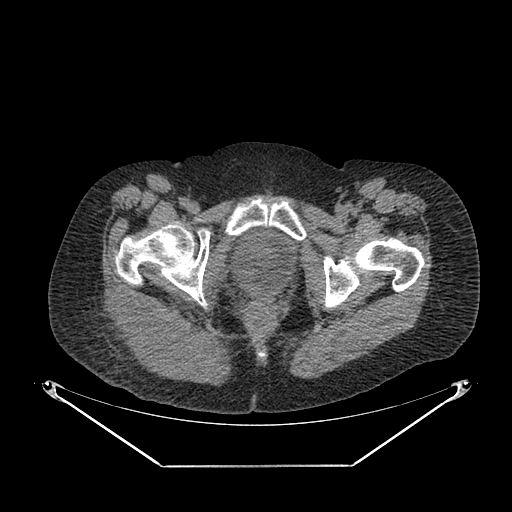
CT of an extremity soft-tissue mass (from a PET/CT study), one axial slice; position 49 of 267 along the scan axis; 140 kVp; soft-tissue window (W 400 / L 40 HU); 512 × 512 image matrix, field of view 500 × 500 mm. Female patient. From the clinical record (not read from this slice): histological type: spindle cell suggestive of myxofibrosarcoma; grade: intermediate; site of the primary tumour: right buttock.
Outlined on this slice (expert contour drawn on MRI and transferred to this co-registered scan by the dataset authors):
- gross tumour volume (mass): box from (x=105, y=299) to (x=186, y=369) px